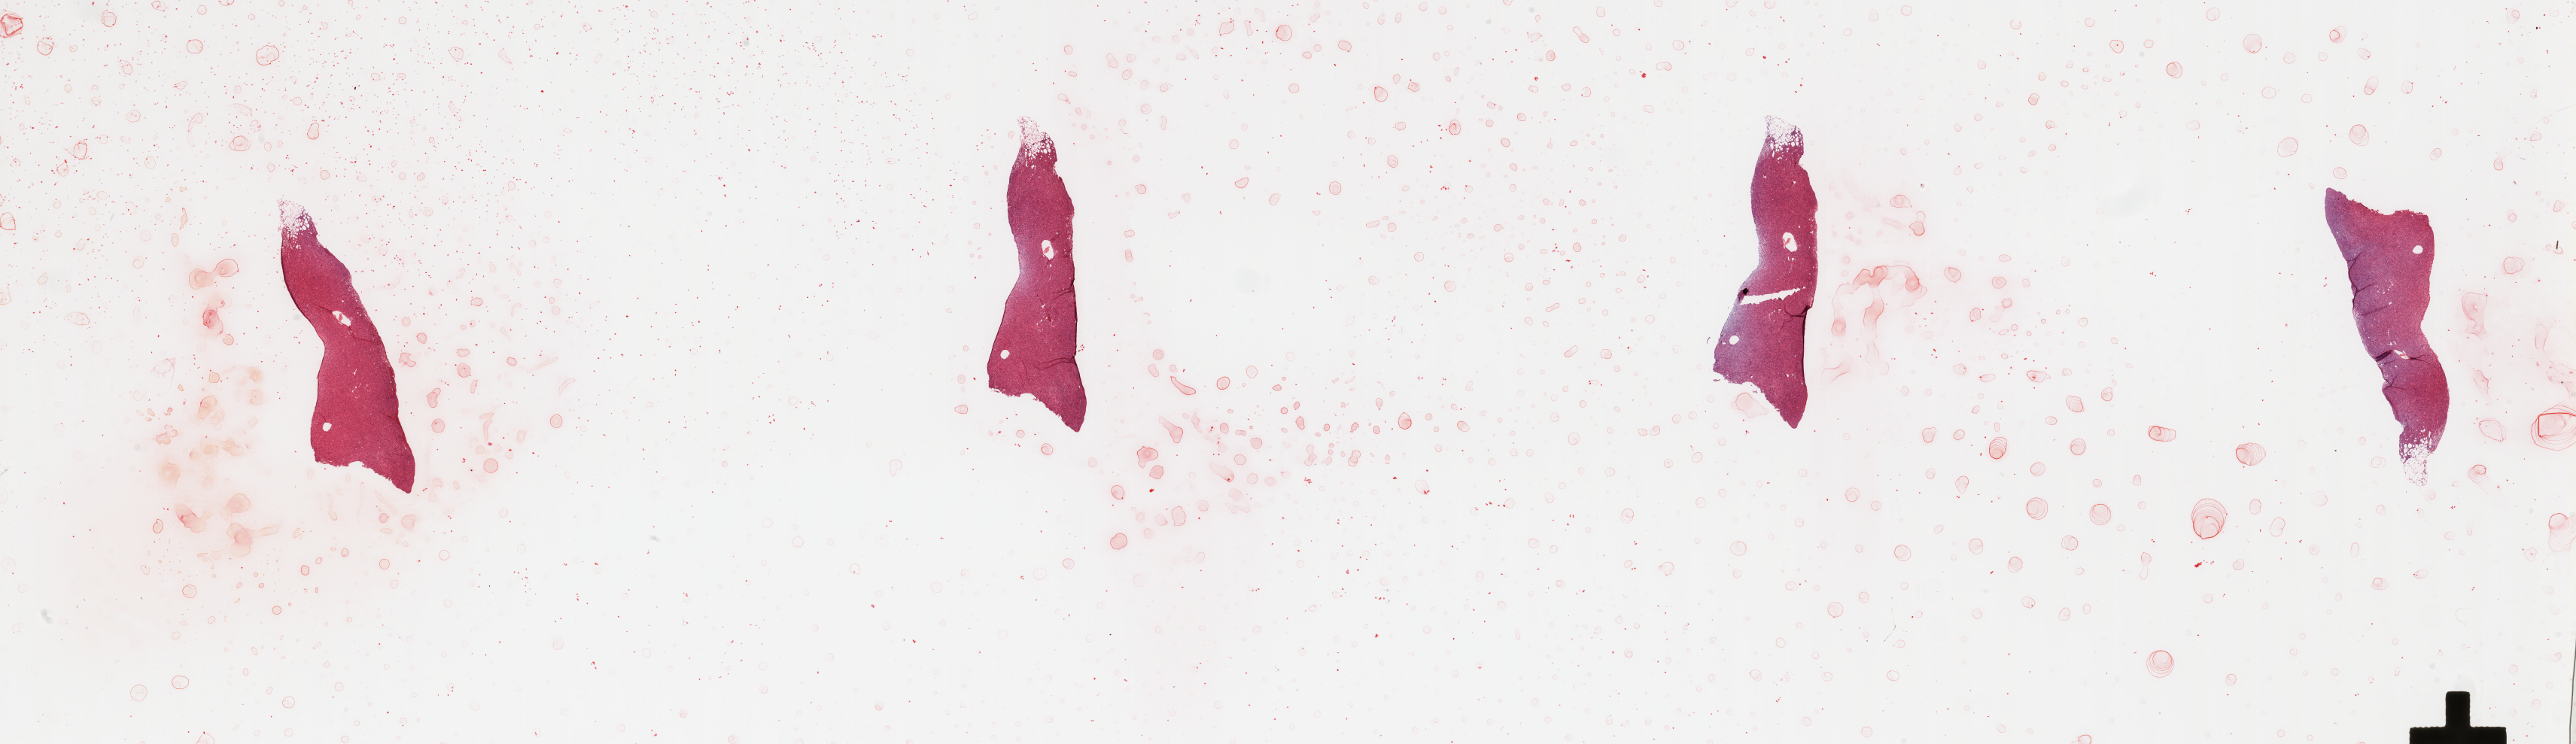
H&E-stained whole-slide image, shown as a low-resolution overview of the whole scanned area (about 54.1 x 15.6 mm). Tumour tissue sample. Female, 75 y/o.
* primary tumour site (as recorded): lower extremity
* patient diagnosis (cohort enrolment): sarcoma (site not recorded at cohort level)